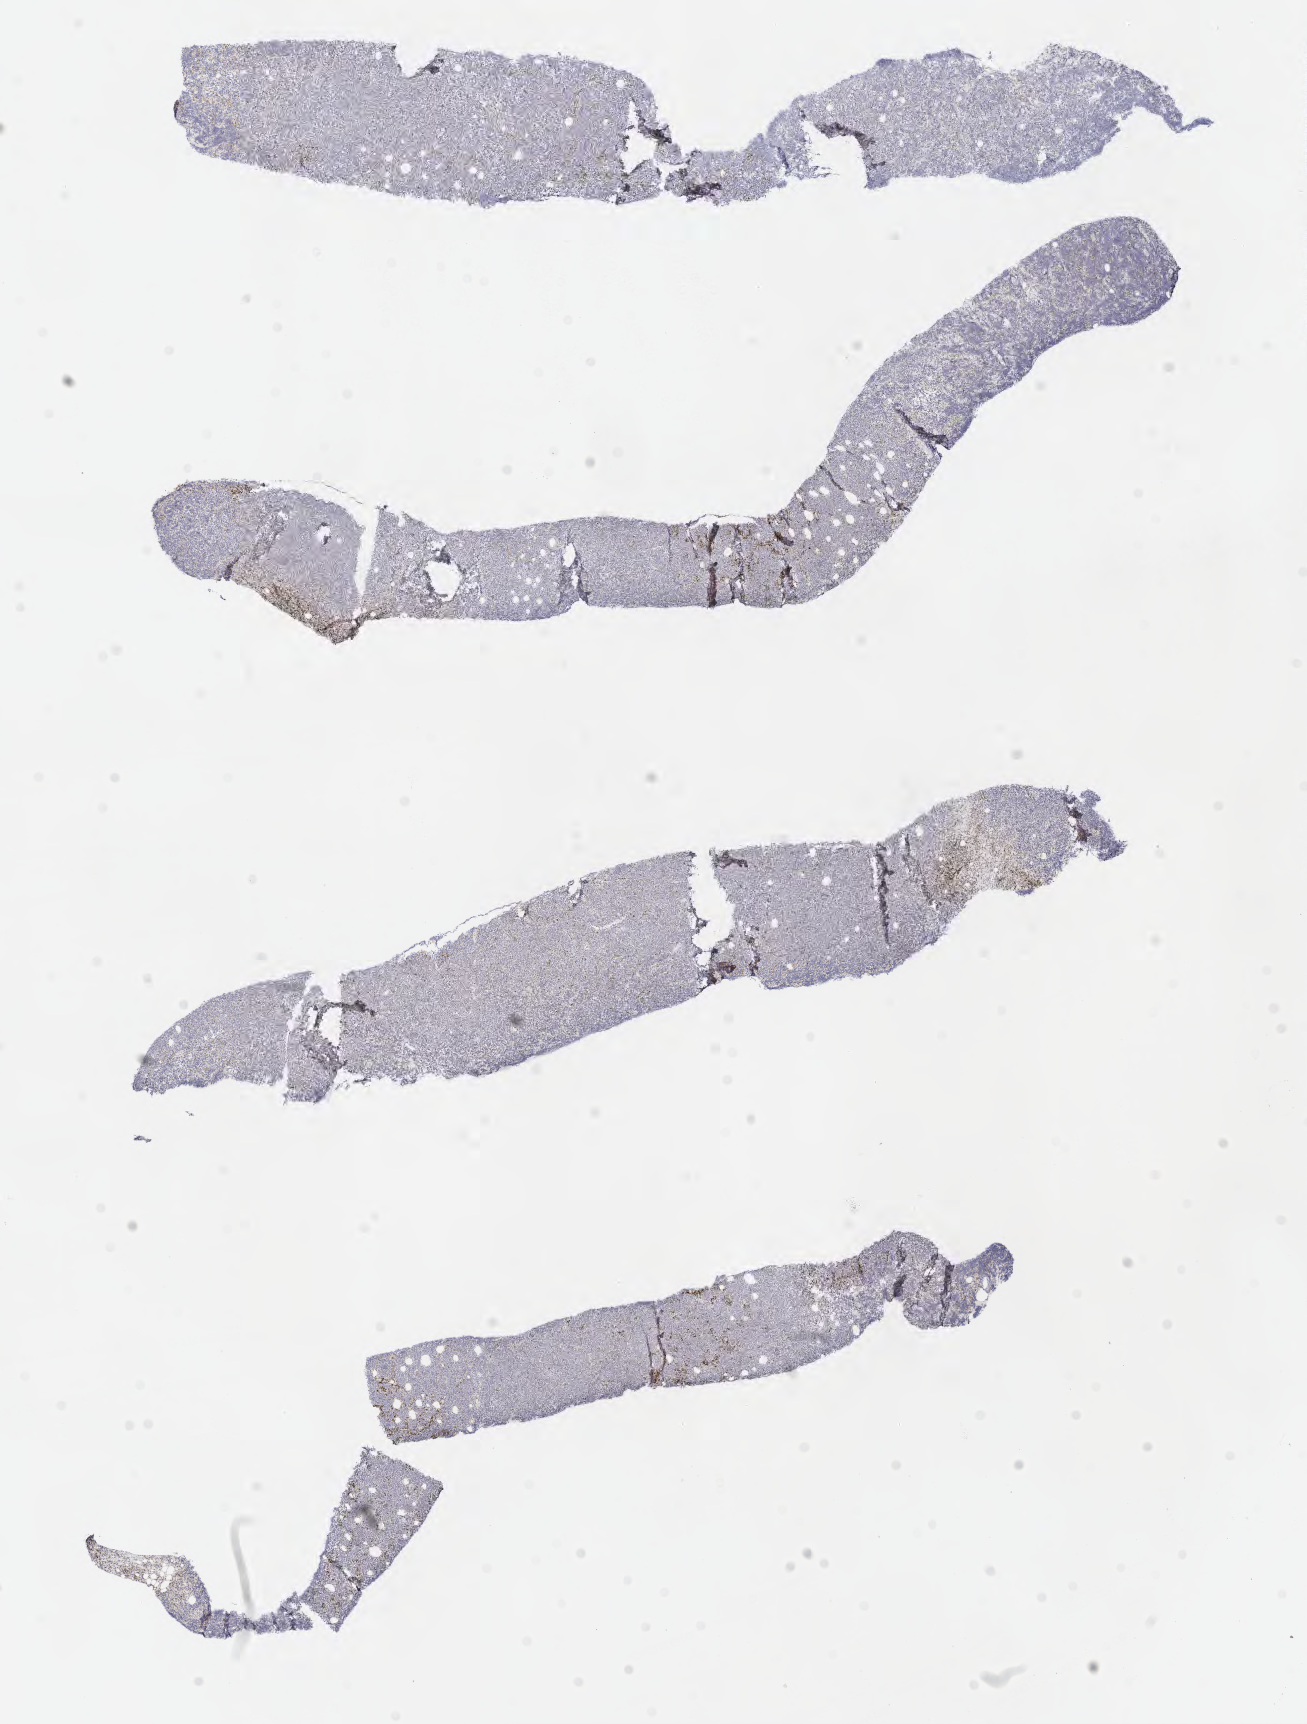
Whole-slide image, immunohistochemical stain for BCL2 — low-resolution overview of the scanned area, about 10.6 x 13.9 mm. Specimen: tumor tissue. Patient male; 69 years old.
Histologic diagnosis: Diffuse large B-cell lymphoma, NOS.